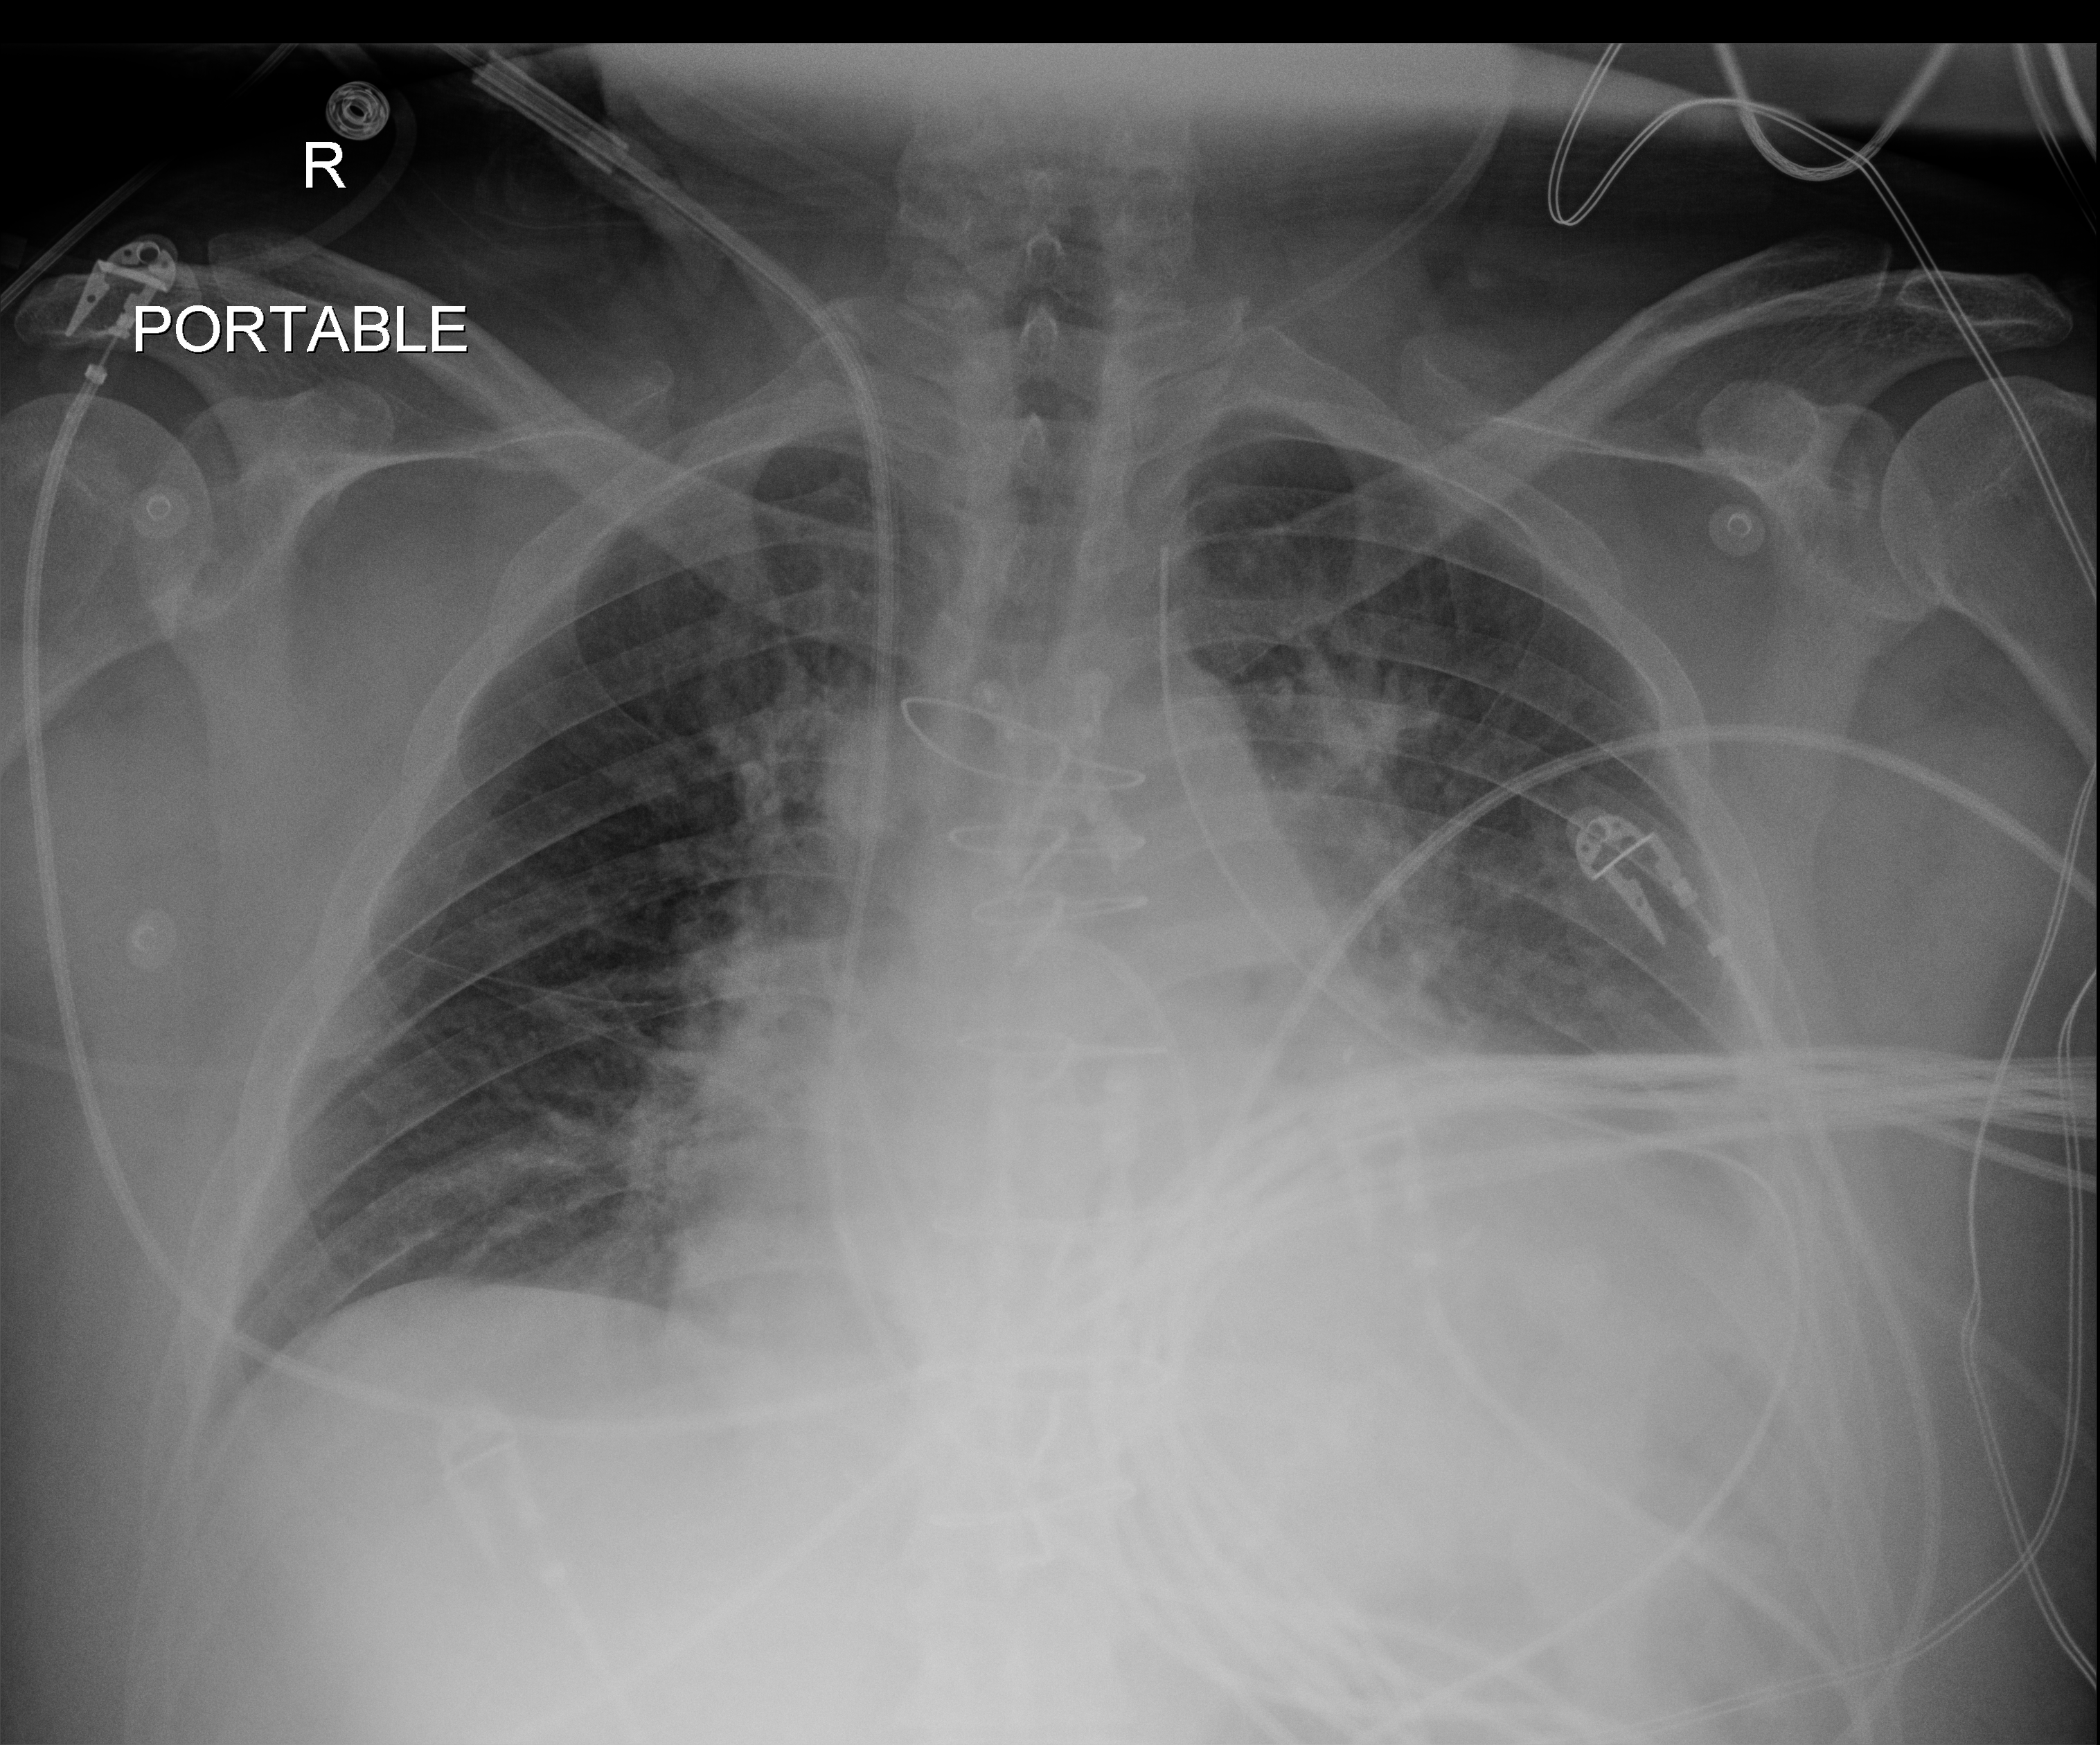
Chest X-ray (portable), anteroposterior (AP) projection. Male patient hospitalised with COVID-19, age 18–59 years.
Admission-level facts for this patient (not findings on this image; timing relative to this image not recorded): mechanically ventilated during this hospital stay: no.